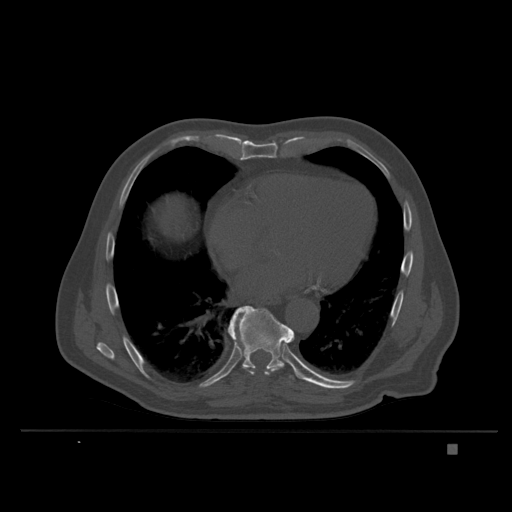
CT including the spine, one axial slice. Bone window (W 1800 / L 400 HU). 512 × 512 image matrix, field of view 434 × 434 mm. Patient: male, 73 years. From the clinical record (not read from this slice): primary cancer: skin.
Outlined on this slice (semi-automatic segmentation, software-assisted and operator-edited):
- T6 vertebra: bounding box (x1, y1, x2, y2) in pixels: (280, 329, 293, 348)
- T8 vertebra: (229, 324, 292, 376)
- T9 vertebra: (228, 306, 304, 380)